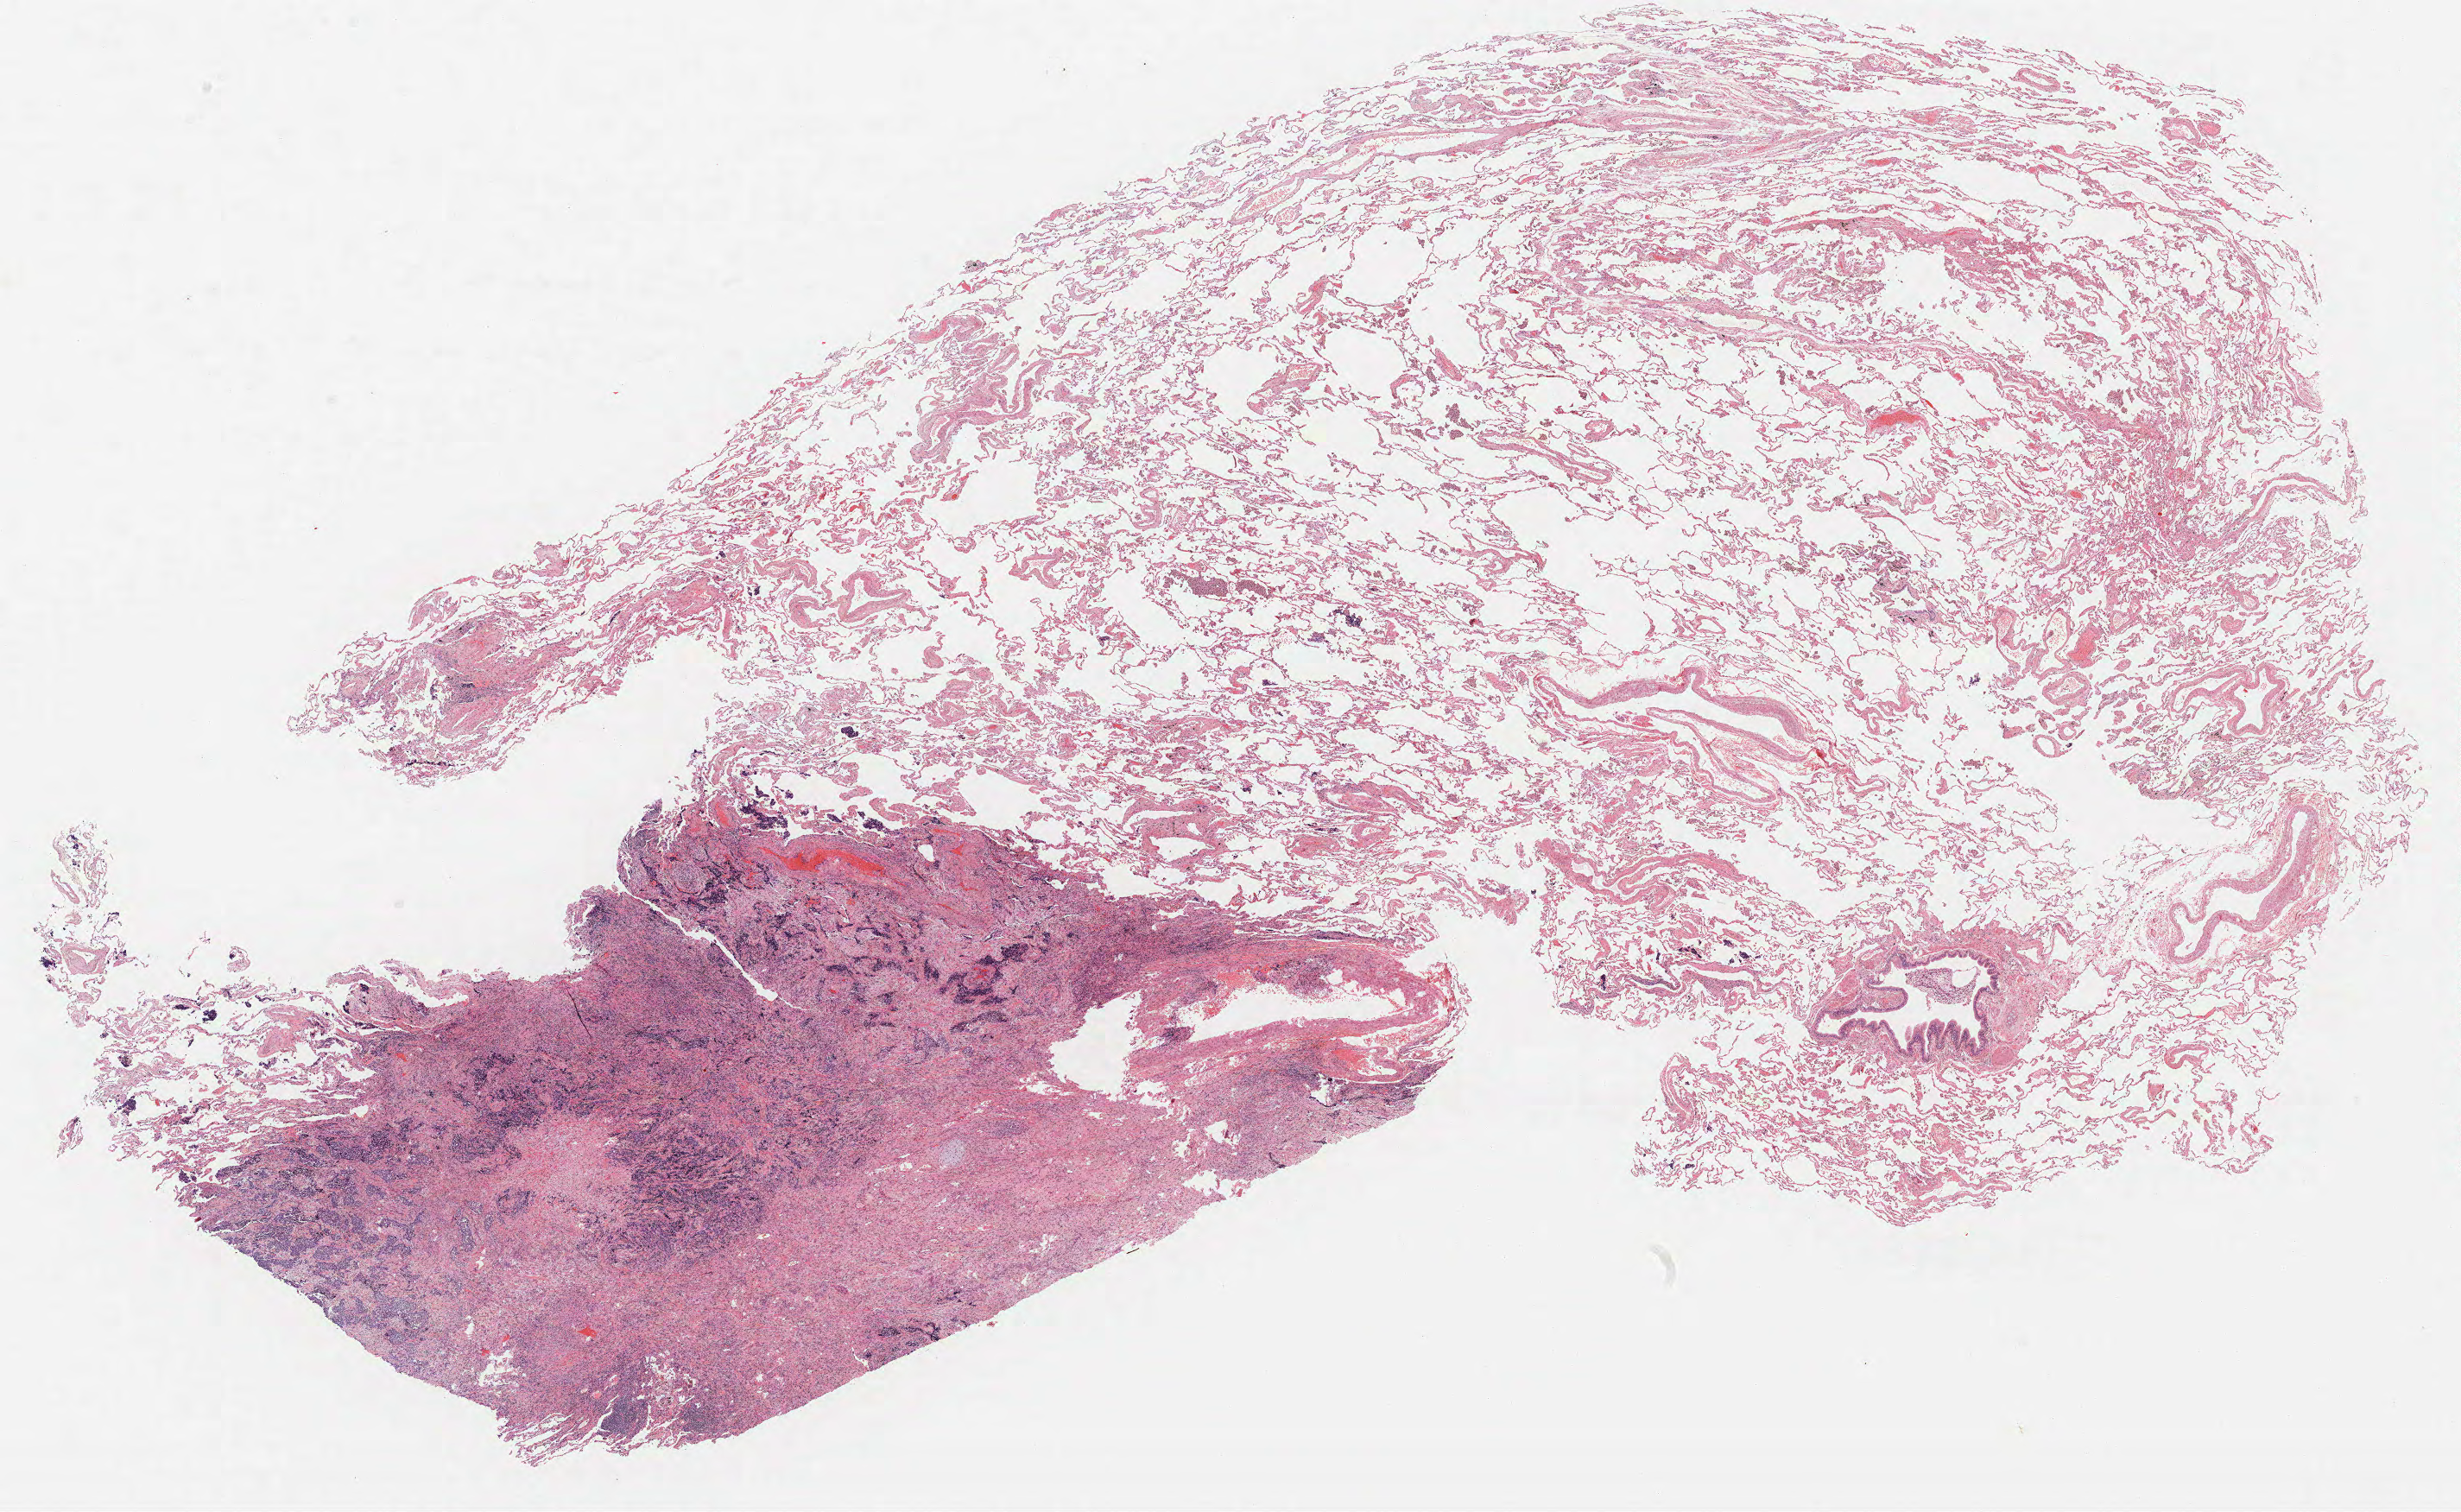
Whole-slide histology image, H&E, shown as a low-resolution overview of the whole scanned area (about 22.8 x 14.0 mm, from a 40x scan). Formalin-fixed paraffin-embedded (FFPE) section. Lung. Male, age 70 at enrolment. Current smoker at enrolment.
Primary tumour location (clinical record): right upper lobe. Tumour size (pathology): 11 mm. Participant's lung-cancer diagnosis: Small cell carcinoma, NOS. Stage (AJCC 6th edition): IA.